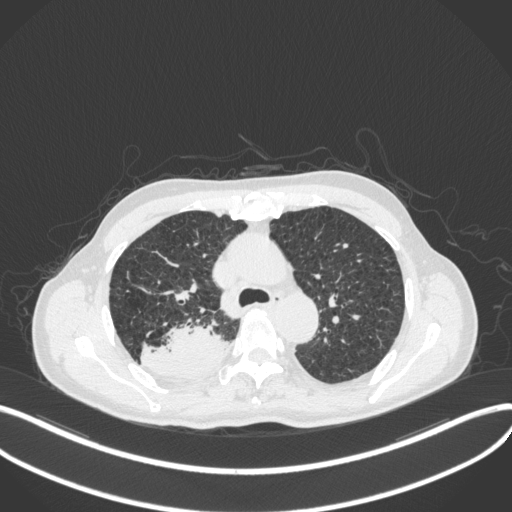
Chest CT, one axial slice; reconstruction kernel B31f; 120 kVp; lung window (W 1500 / L -600 HU); 1 mm slice thickness; 512 × 512 image matrix, field of view 400 × 400 mm. Patient: male, 79 years. Case-level facts recorded for this patient, not image findings: clinical TNM (as recorded): T3 N0 M0.
Outlined on this slice (bounding box drawn by a radiologist):
- lung tumour (recorded histology: adenocarcinoma): box from (x=144, y=323) to (x=231, y=384) px